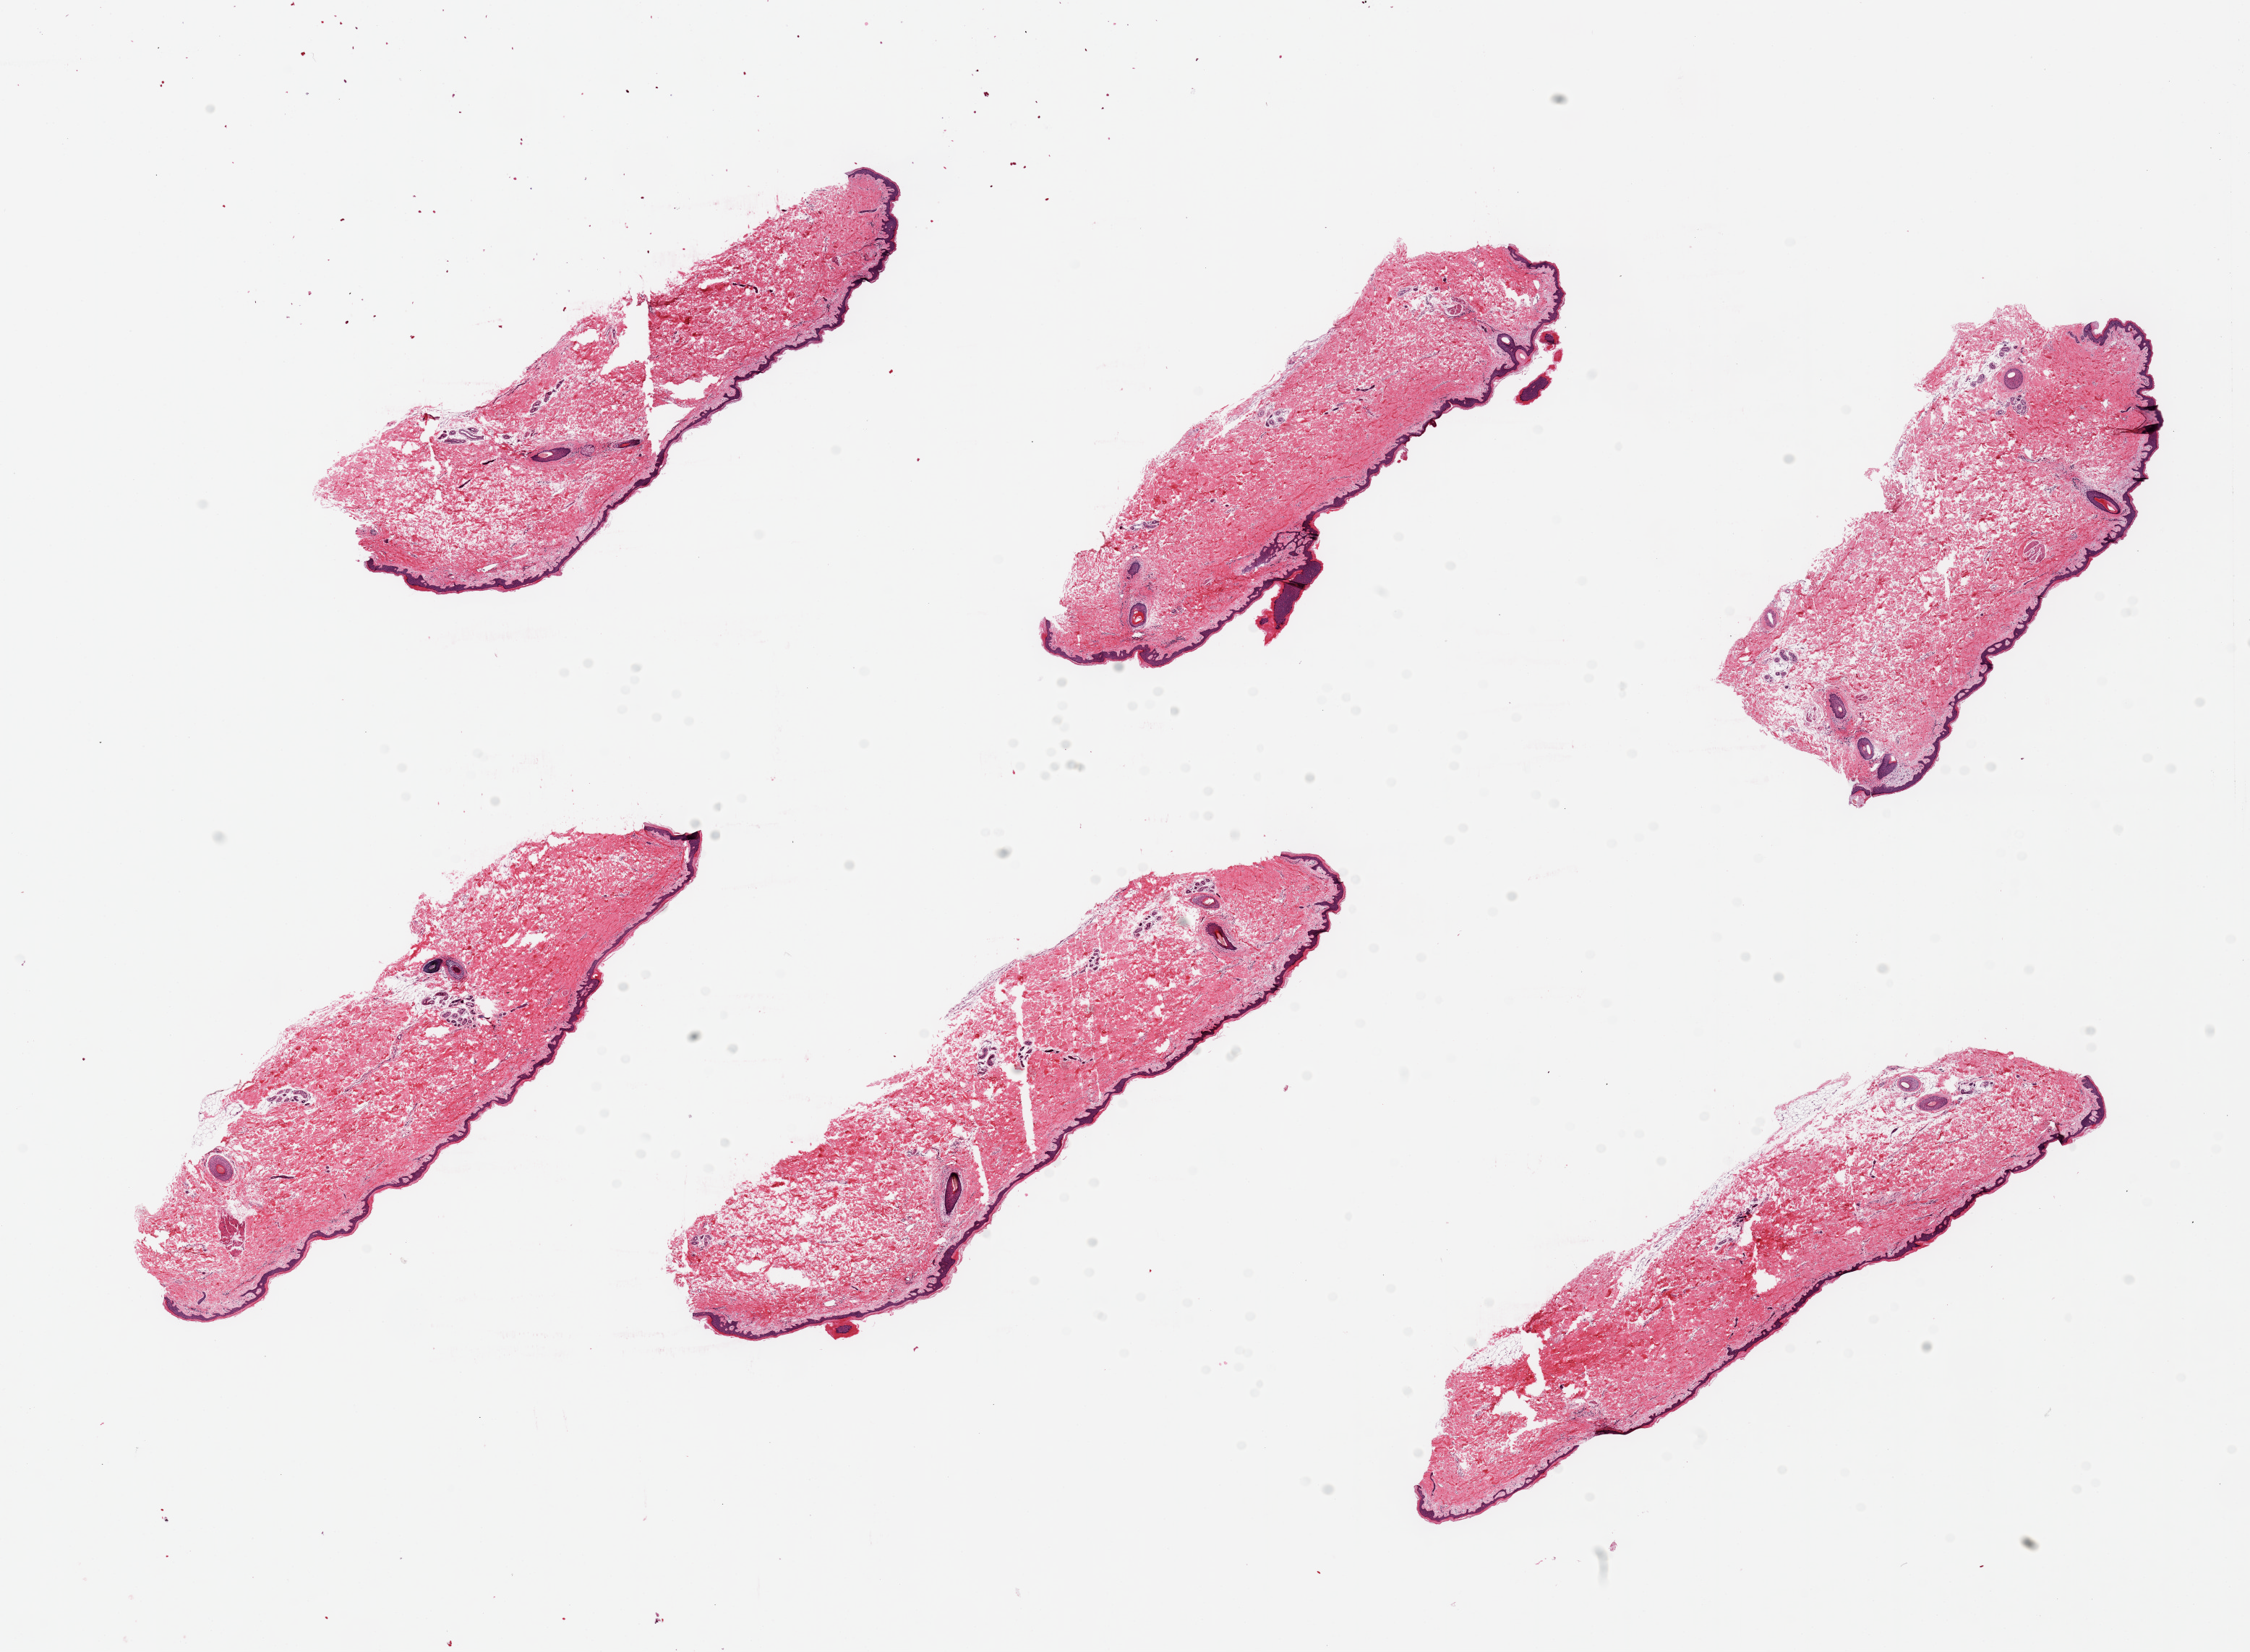
Digitized haematoxylin and eosin-stained section, brightfield, a low-resolution overview of the entire scanned area, about 24.6 x 18.1 mm (acquisition: 20x scan). PAXgene-fixed, paraffin-embedded tissue. Sampled site (target tissue): skin of suprapubic region. Donor tissue sample. Donor: male.
Pathologist's review note for this sample: 6 pieces ~9x3, squamous epithelium is ~1.5-2% thickness.